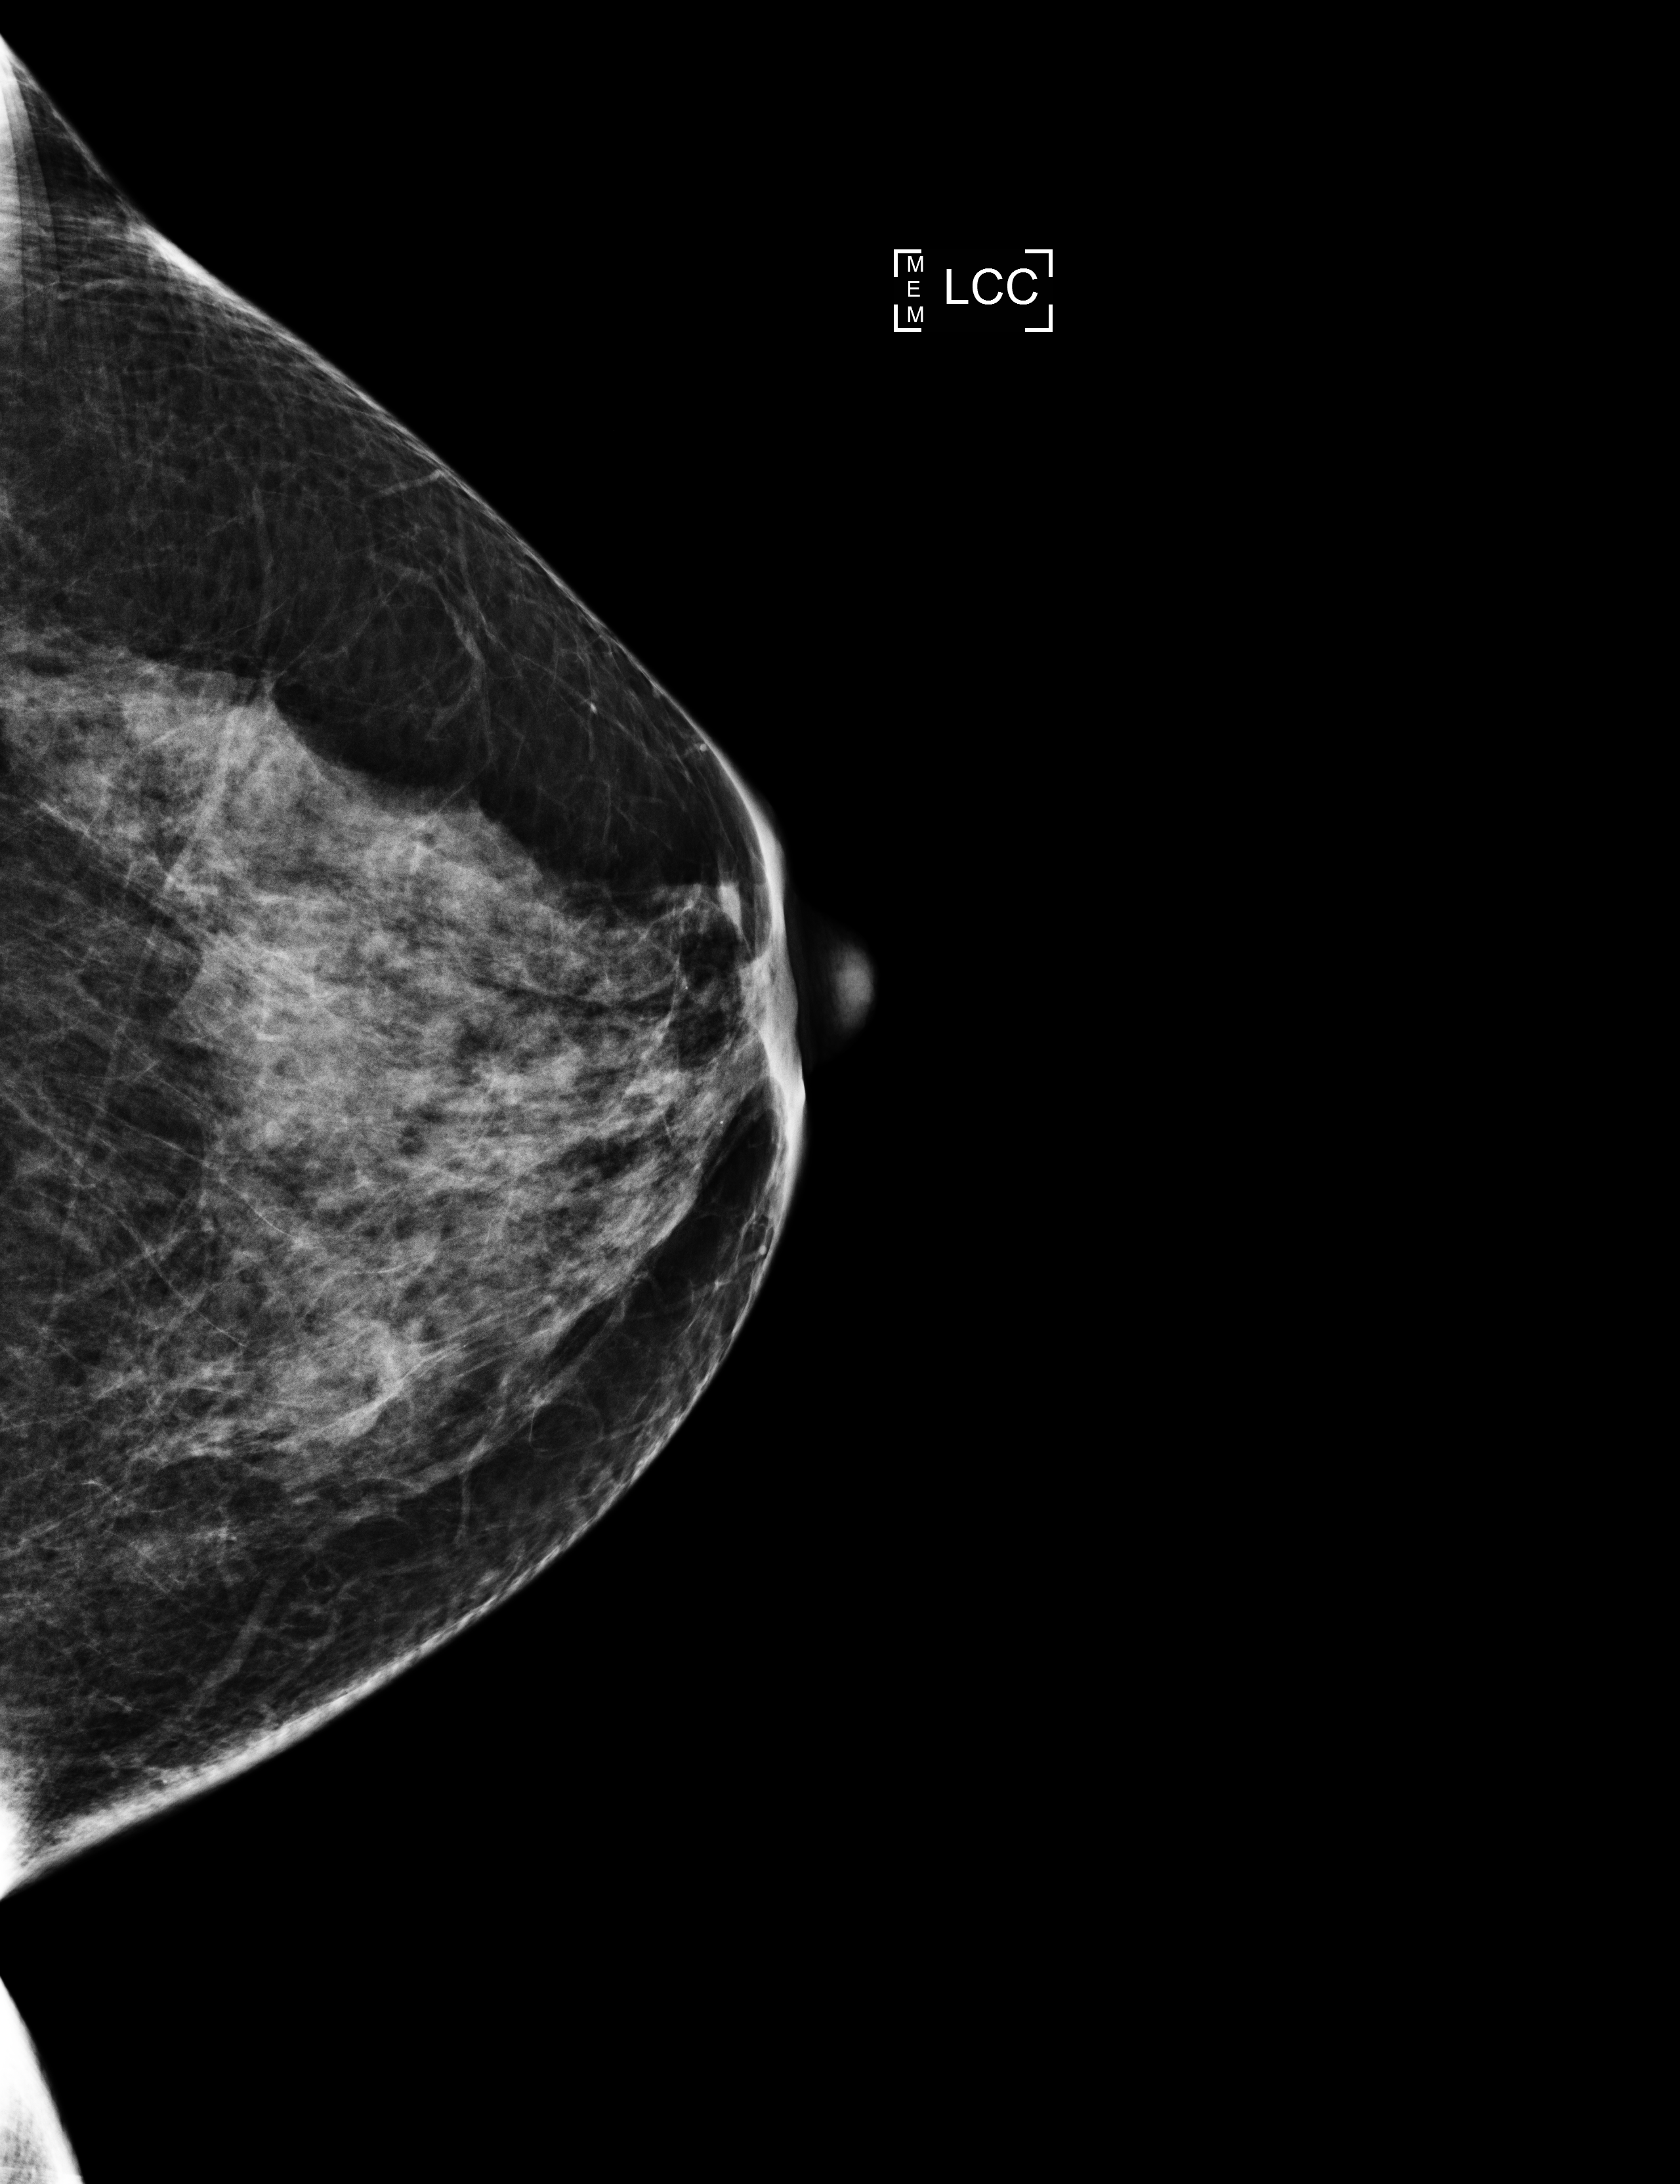
Full-field digital mammogram (FFDM), left breast, craniocaudal (CC) view, screening examination, system: Selenia Dimensions. Female patient, age 57 years.
- BI-RADS breast density category at the screening exam (both breasts, scale 1–4): 3
- final BI-RADS assessment for this screening round (tomosynthesis exam, both breasts): category 1
- recall: no recall after this screen